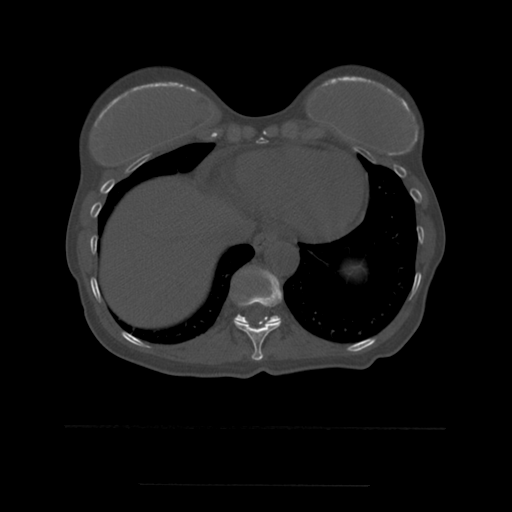
CT including the spine, one axial slice; slice 294 of 544 in the series (ordered by position); bone window (W 1800 / L 400 HU); 1.25 mm slice thickness; 512 × 512 image matrix. Patient age 58 years. From the clinical record (not read from this slice): primary cancer: lung.
Annotated regions visible in this slice (semi-automatic segmentation, software-assisted and operator-edited):
- T10 vertebra: bounding box (x1, y1, x2, y2) in pixels: (235, 269, 283, 361)
- T11 vertebra: (234, 270, 281, 324)